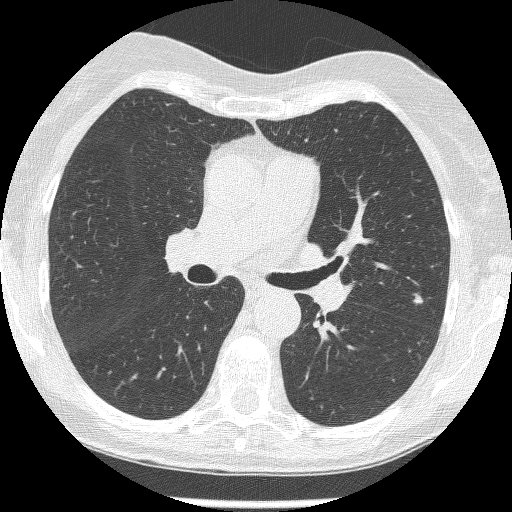
Chest CT (low-dose screening protocol), one axial image. Second annual screen. Lung window (W 1500 / L -600 HU). Slice 165 of 250 in the series. Female participant, aged 60 years at enrolment.
• Lesion marked by an expert reader, bounding box <401,285,438,317> (left, top, right, bottom; pixels).
• The screening reader recorded 2 non-calcified nodules or masses ≥4 mm on this exam (left upper lobe, left upper lobe); which of them this box marks is not recorded.
• Official screen result: positive, change unspecified: nodule(s) >= 4 mm or enlarging nodule(s), mass(es), or other non-specific abnormalities suspicious for lung cancer.
• Participant outcome: lung cancer diagnosed 428 days after this screen — adenocarcinoma, NOS, left upper lobe, moderately differentiated (G2), stage IA (AJCC 6th edition), 6 mm at pathology.